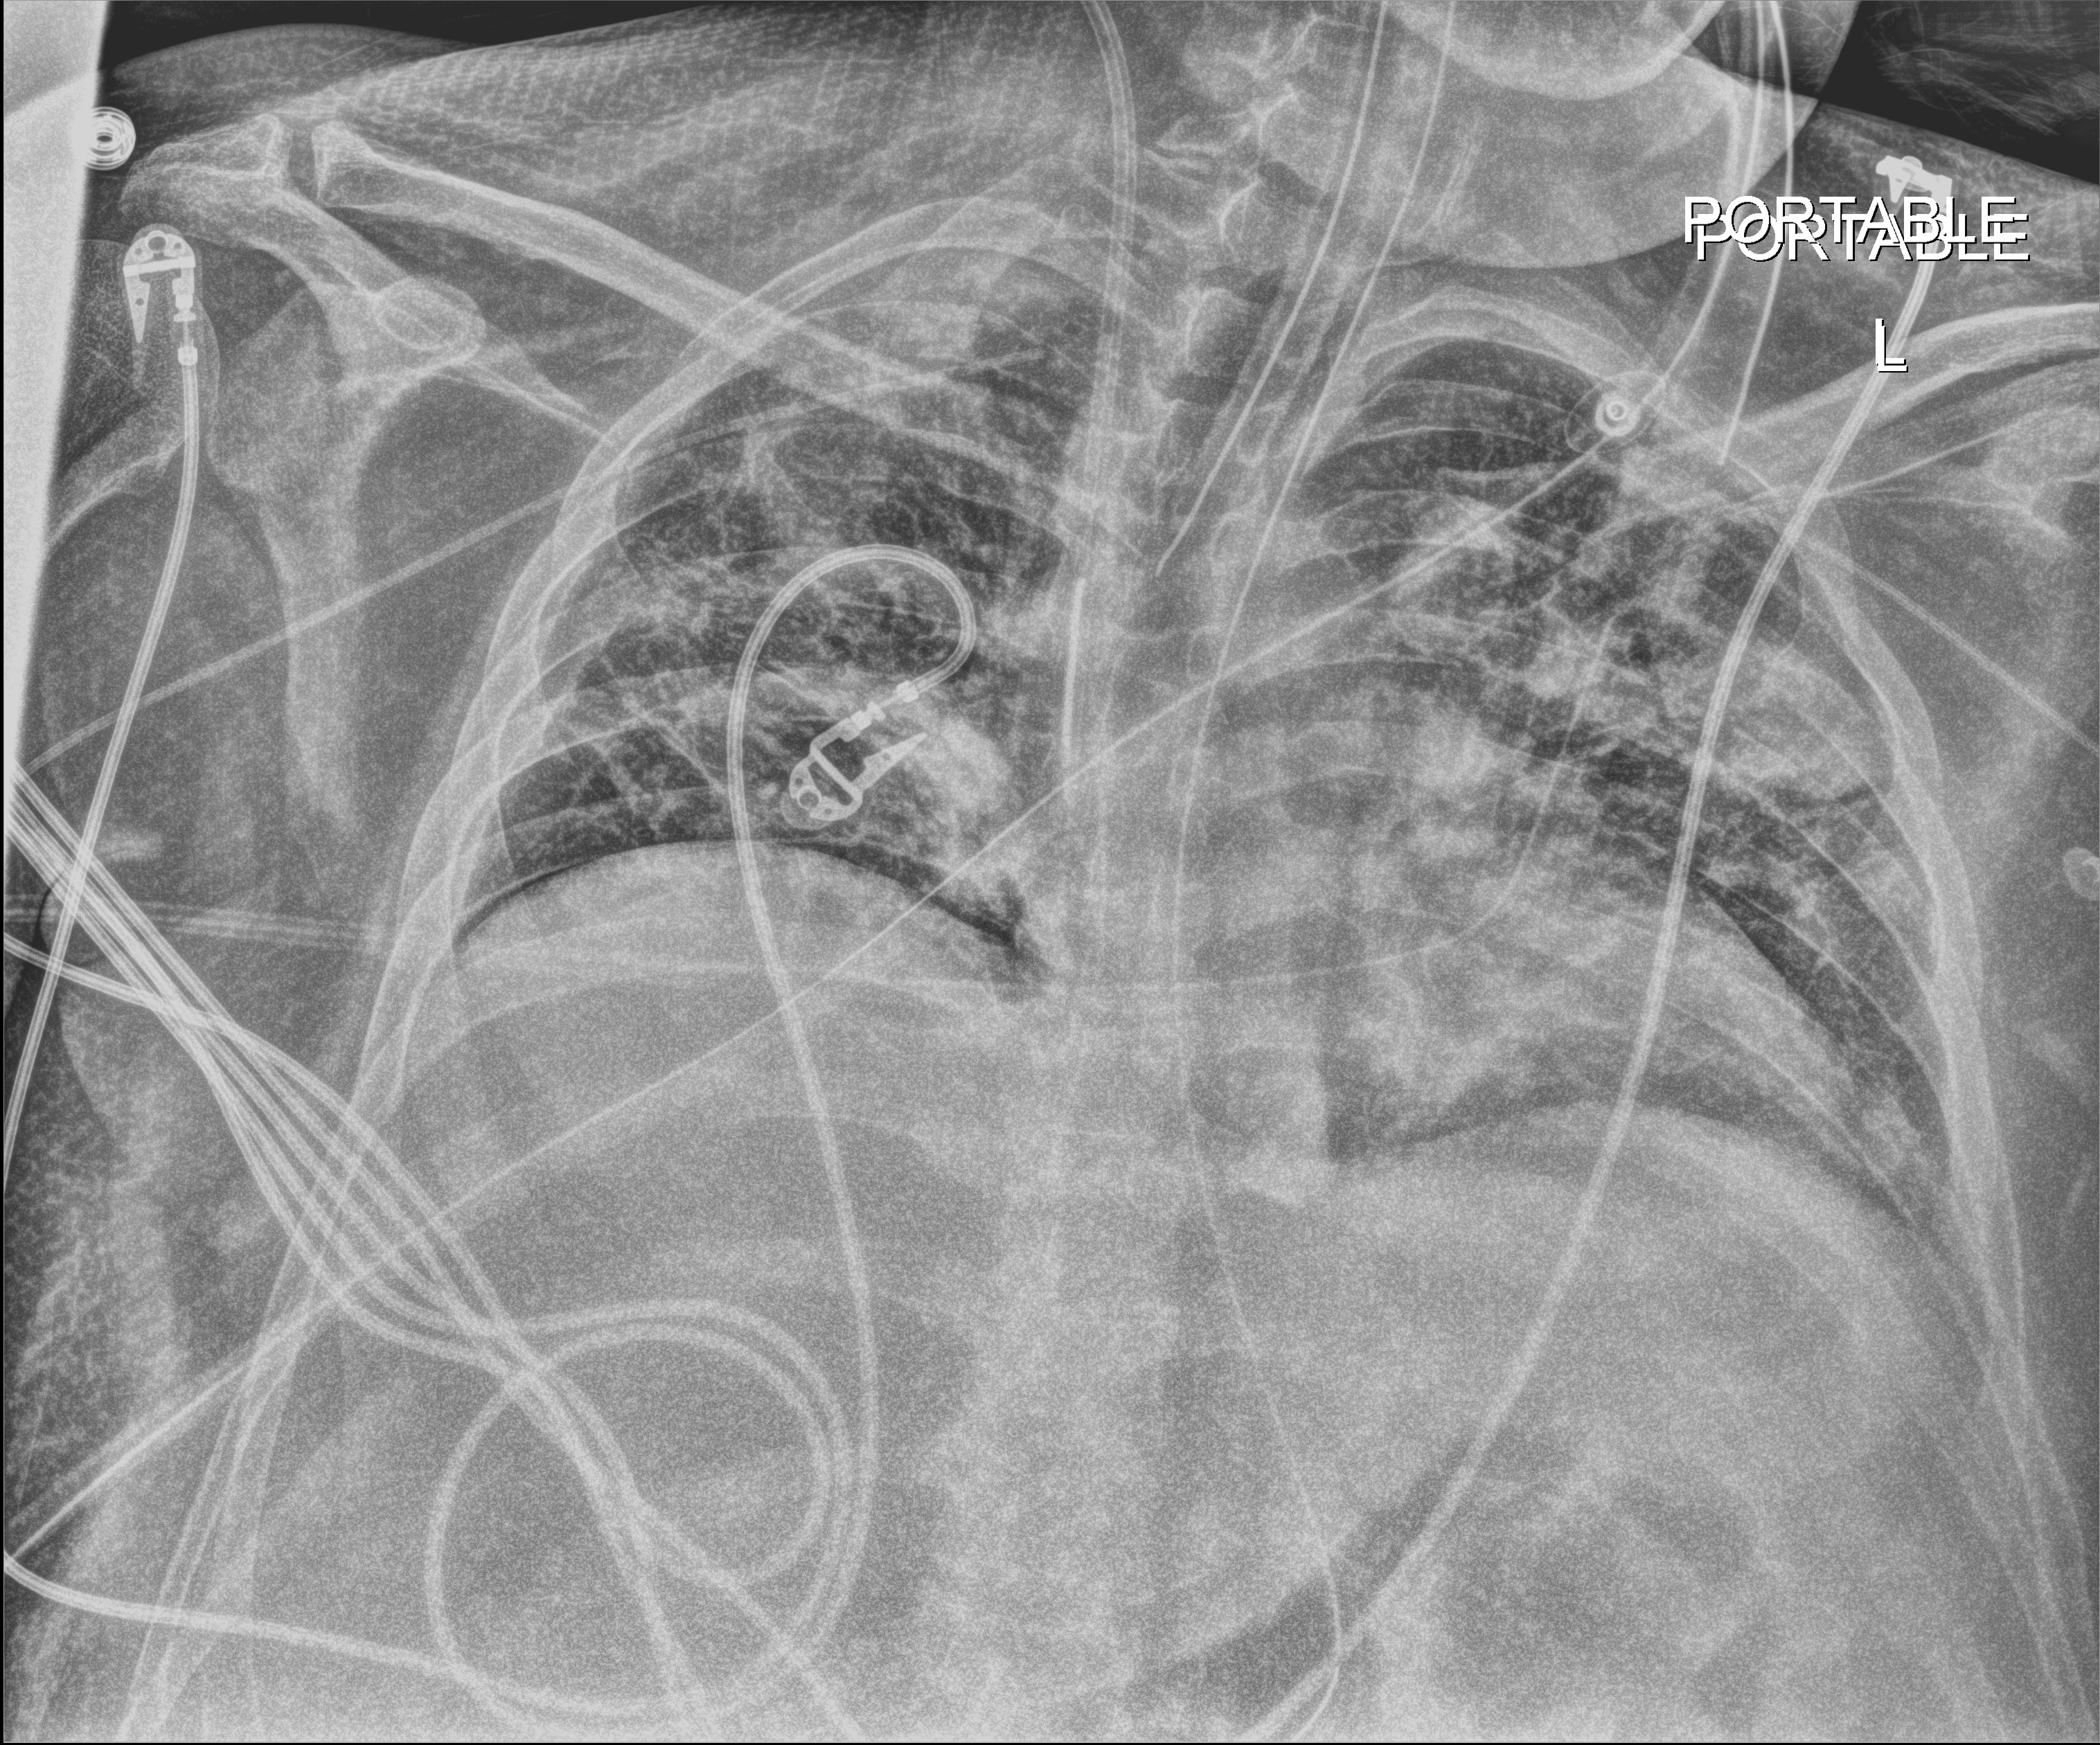
Chest radiograph, anteroposterior (AP) projection. Patient hospitalised with COVID-19, aged 18–59 years.
Hospital-stay facts (about this admission, not read from this image; timing relative to this image not recorded): admitted to intensive care during this hospital stay: yes; length of hospital stay: 50 days.